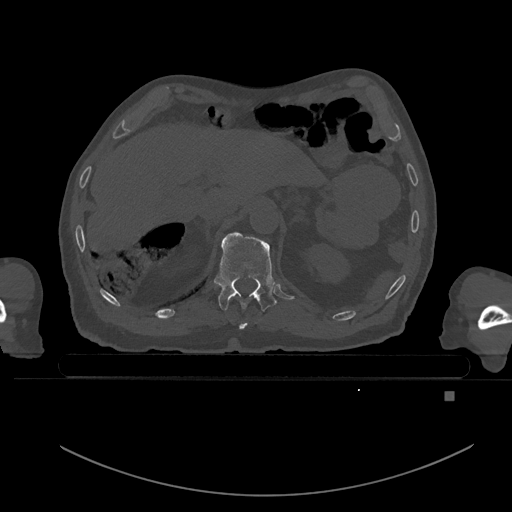
CT including the spine, one axial slice; position 39 of 969 along the scan axis; bone window (W 1800 / L 400 HU); 0.5 mm slice thickness; 512 × 512 image matrix, field of view 456 × 456 mm. Patient: male, 82 years. From the clinical record (not read from this slice): primary cancer: prostate.
Structures marked on this image (semi-automatic segmentation, software-assisted and operator-edited):
- T10 vertebra: bounding box [x1, y1, x2, y2] px = [239, 321, 248, 329]
- T11 vertebra: [214, 232, 277, 312]